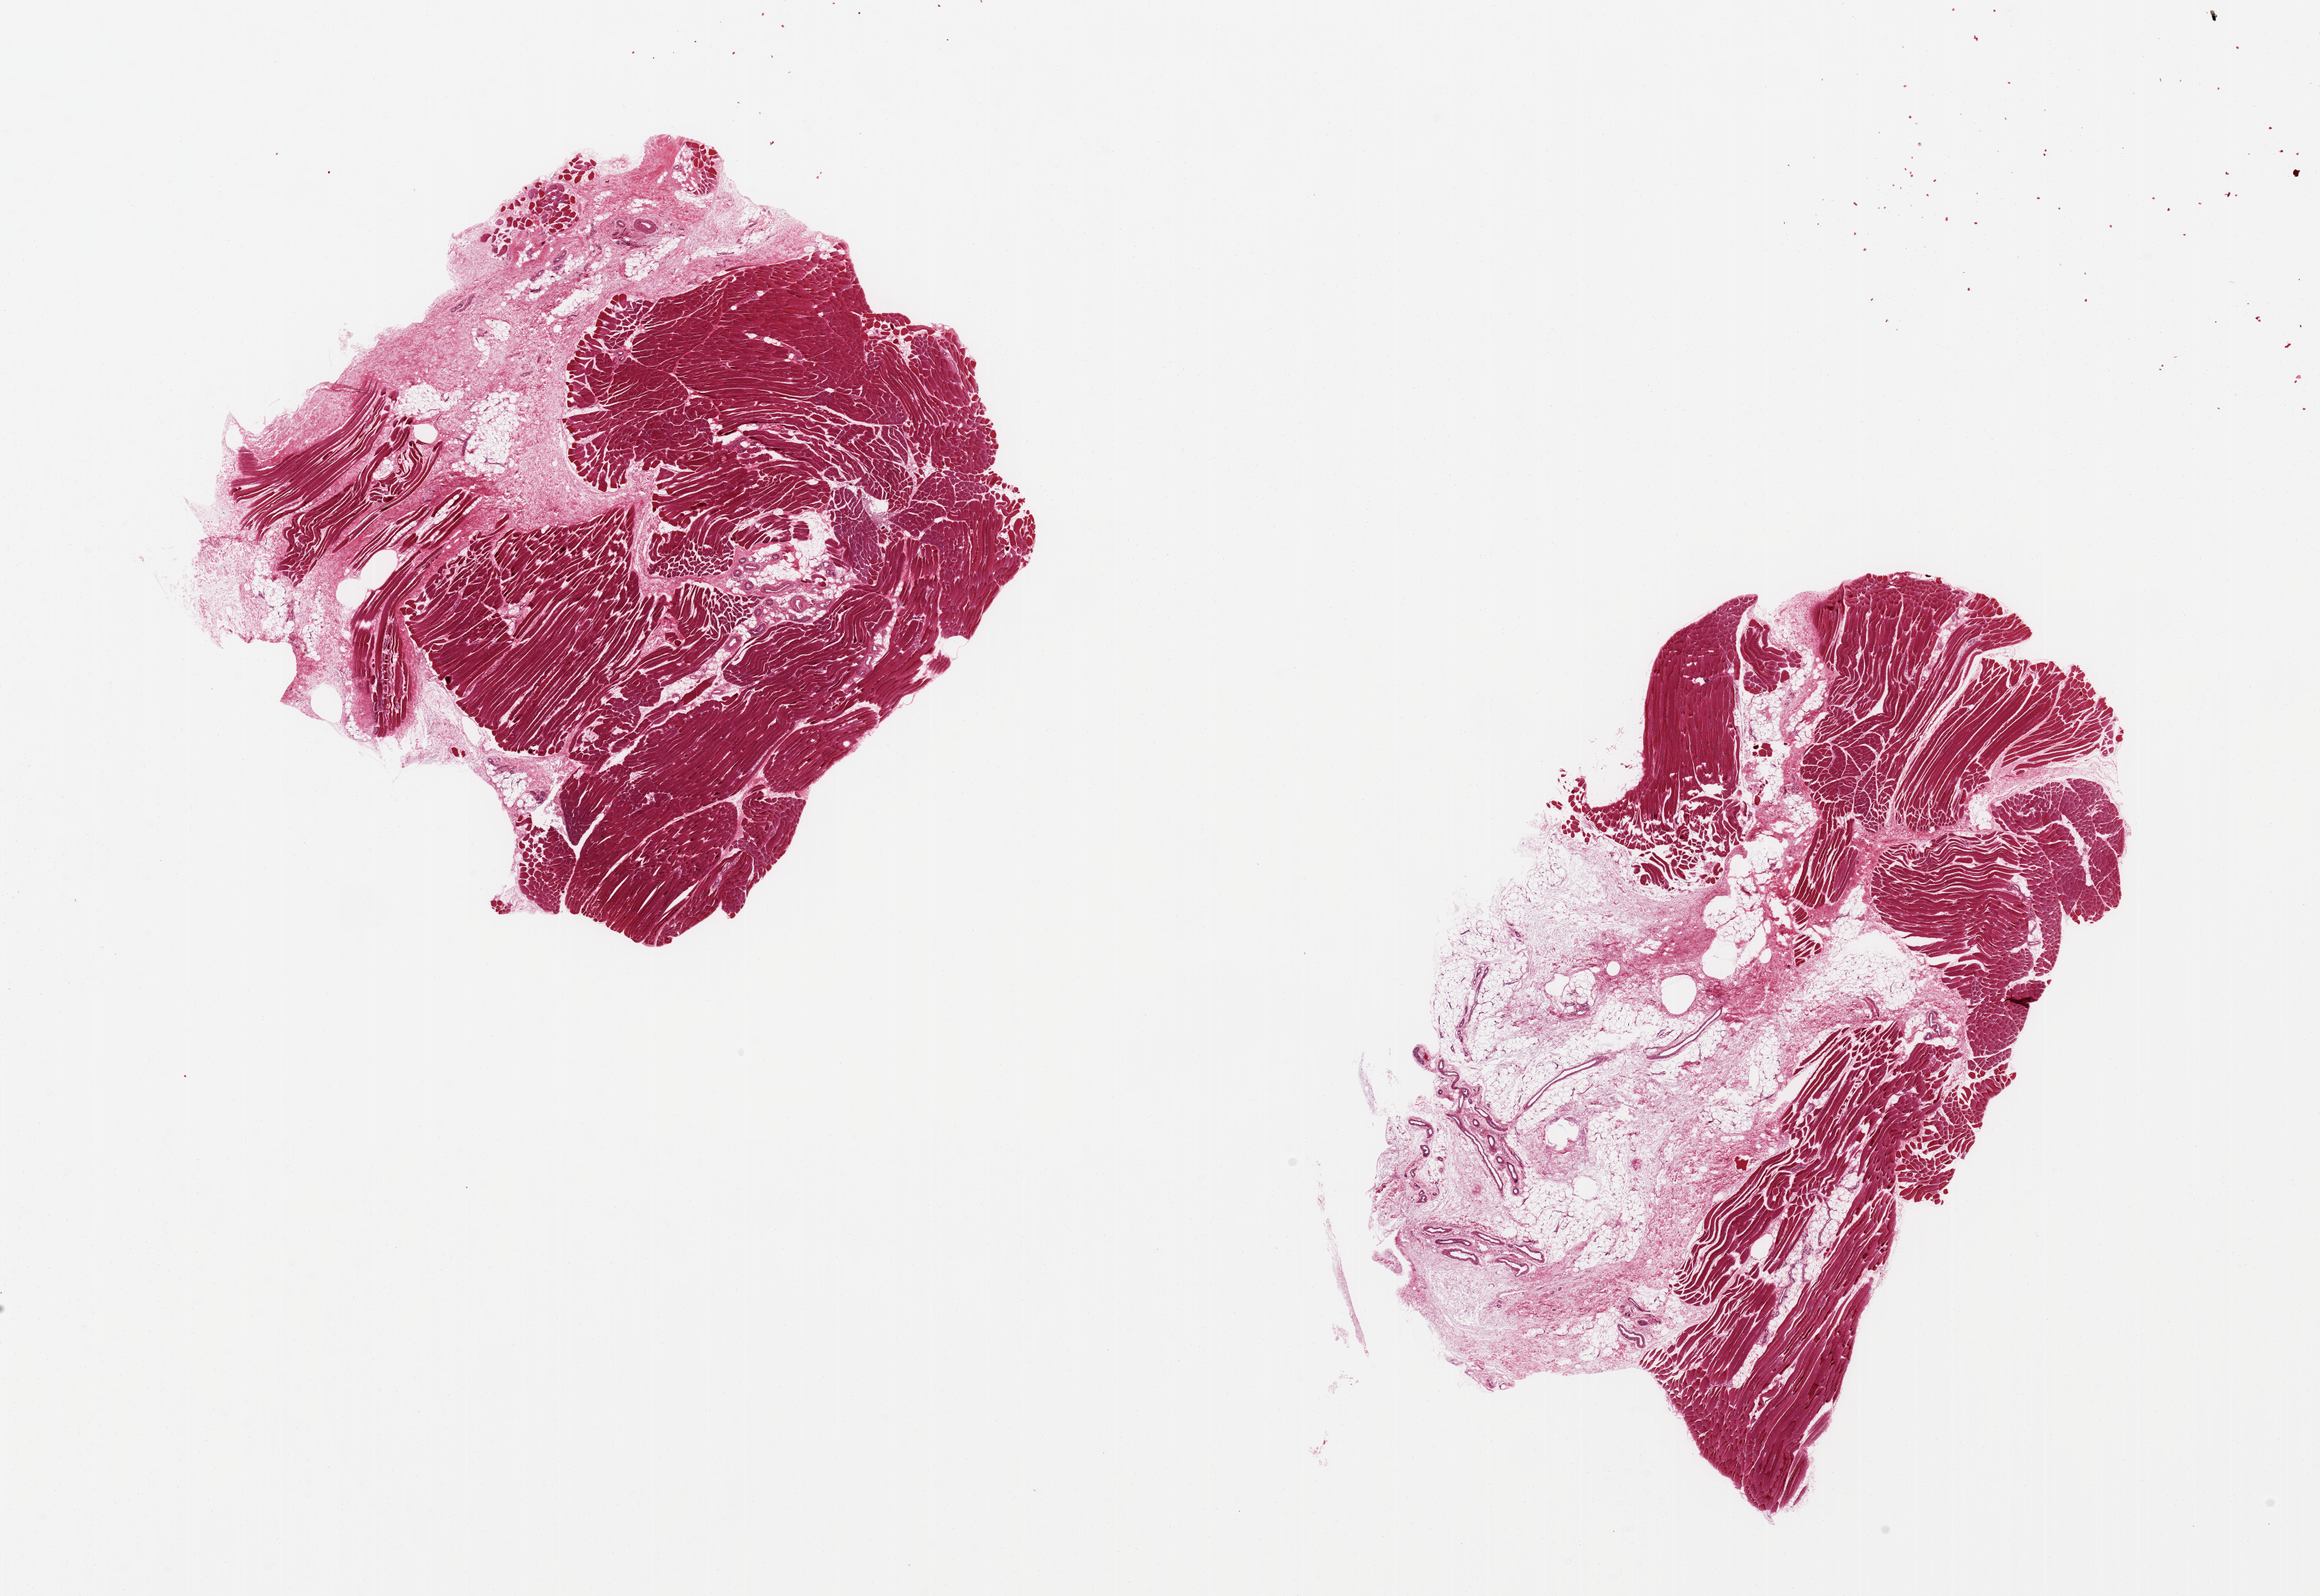
Digitized haematoxylin and eosin-stained section — low-resolution overview of the scanned area, about 24.6 x 16.9 mm (from a 20x scan), PAXgene-fixed paraffin-embedded (PFPE) section, sampled site (target tissue): skeletal muscle, tissue donor sample. Donor sex: male.
• review note (as recorded): 2 pieces, ~7x7 & 9x5 mm, about 60% and 25% fat and stroma